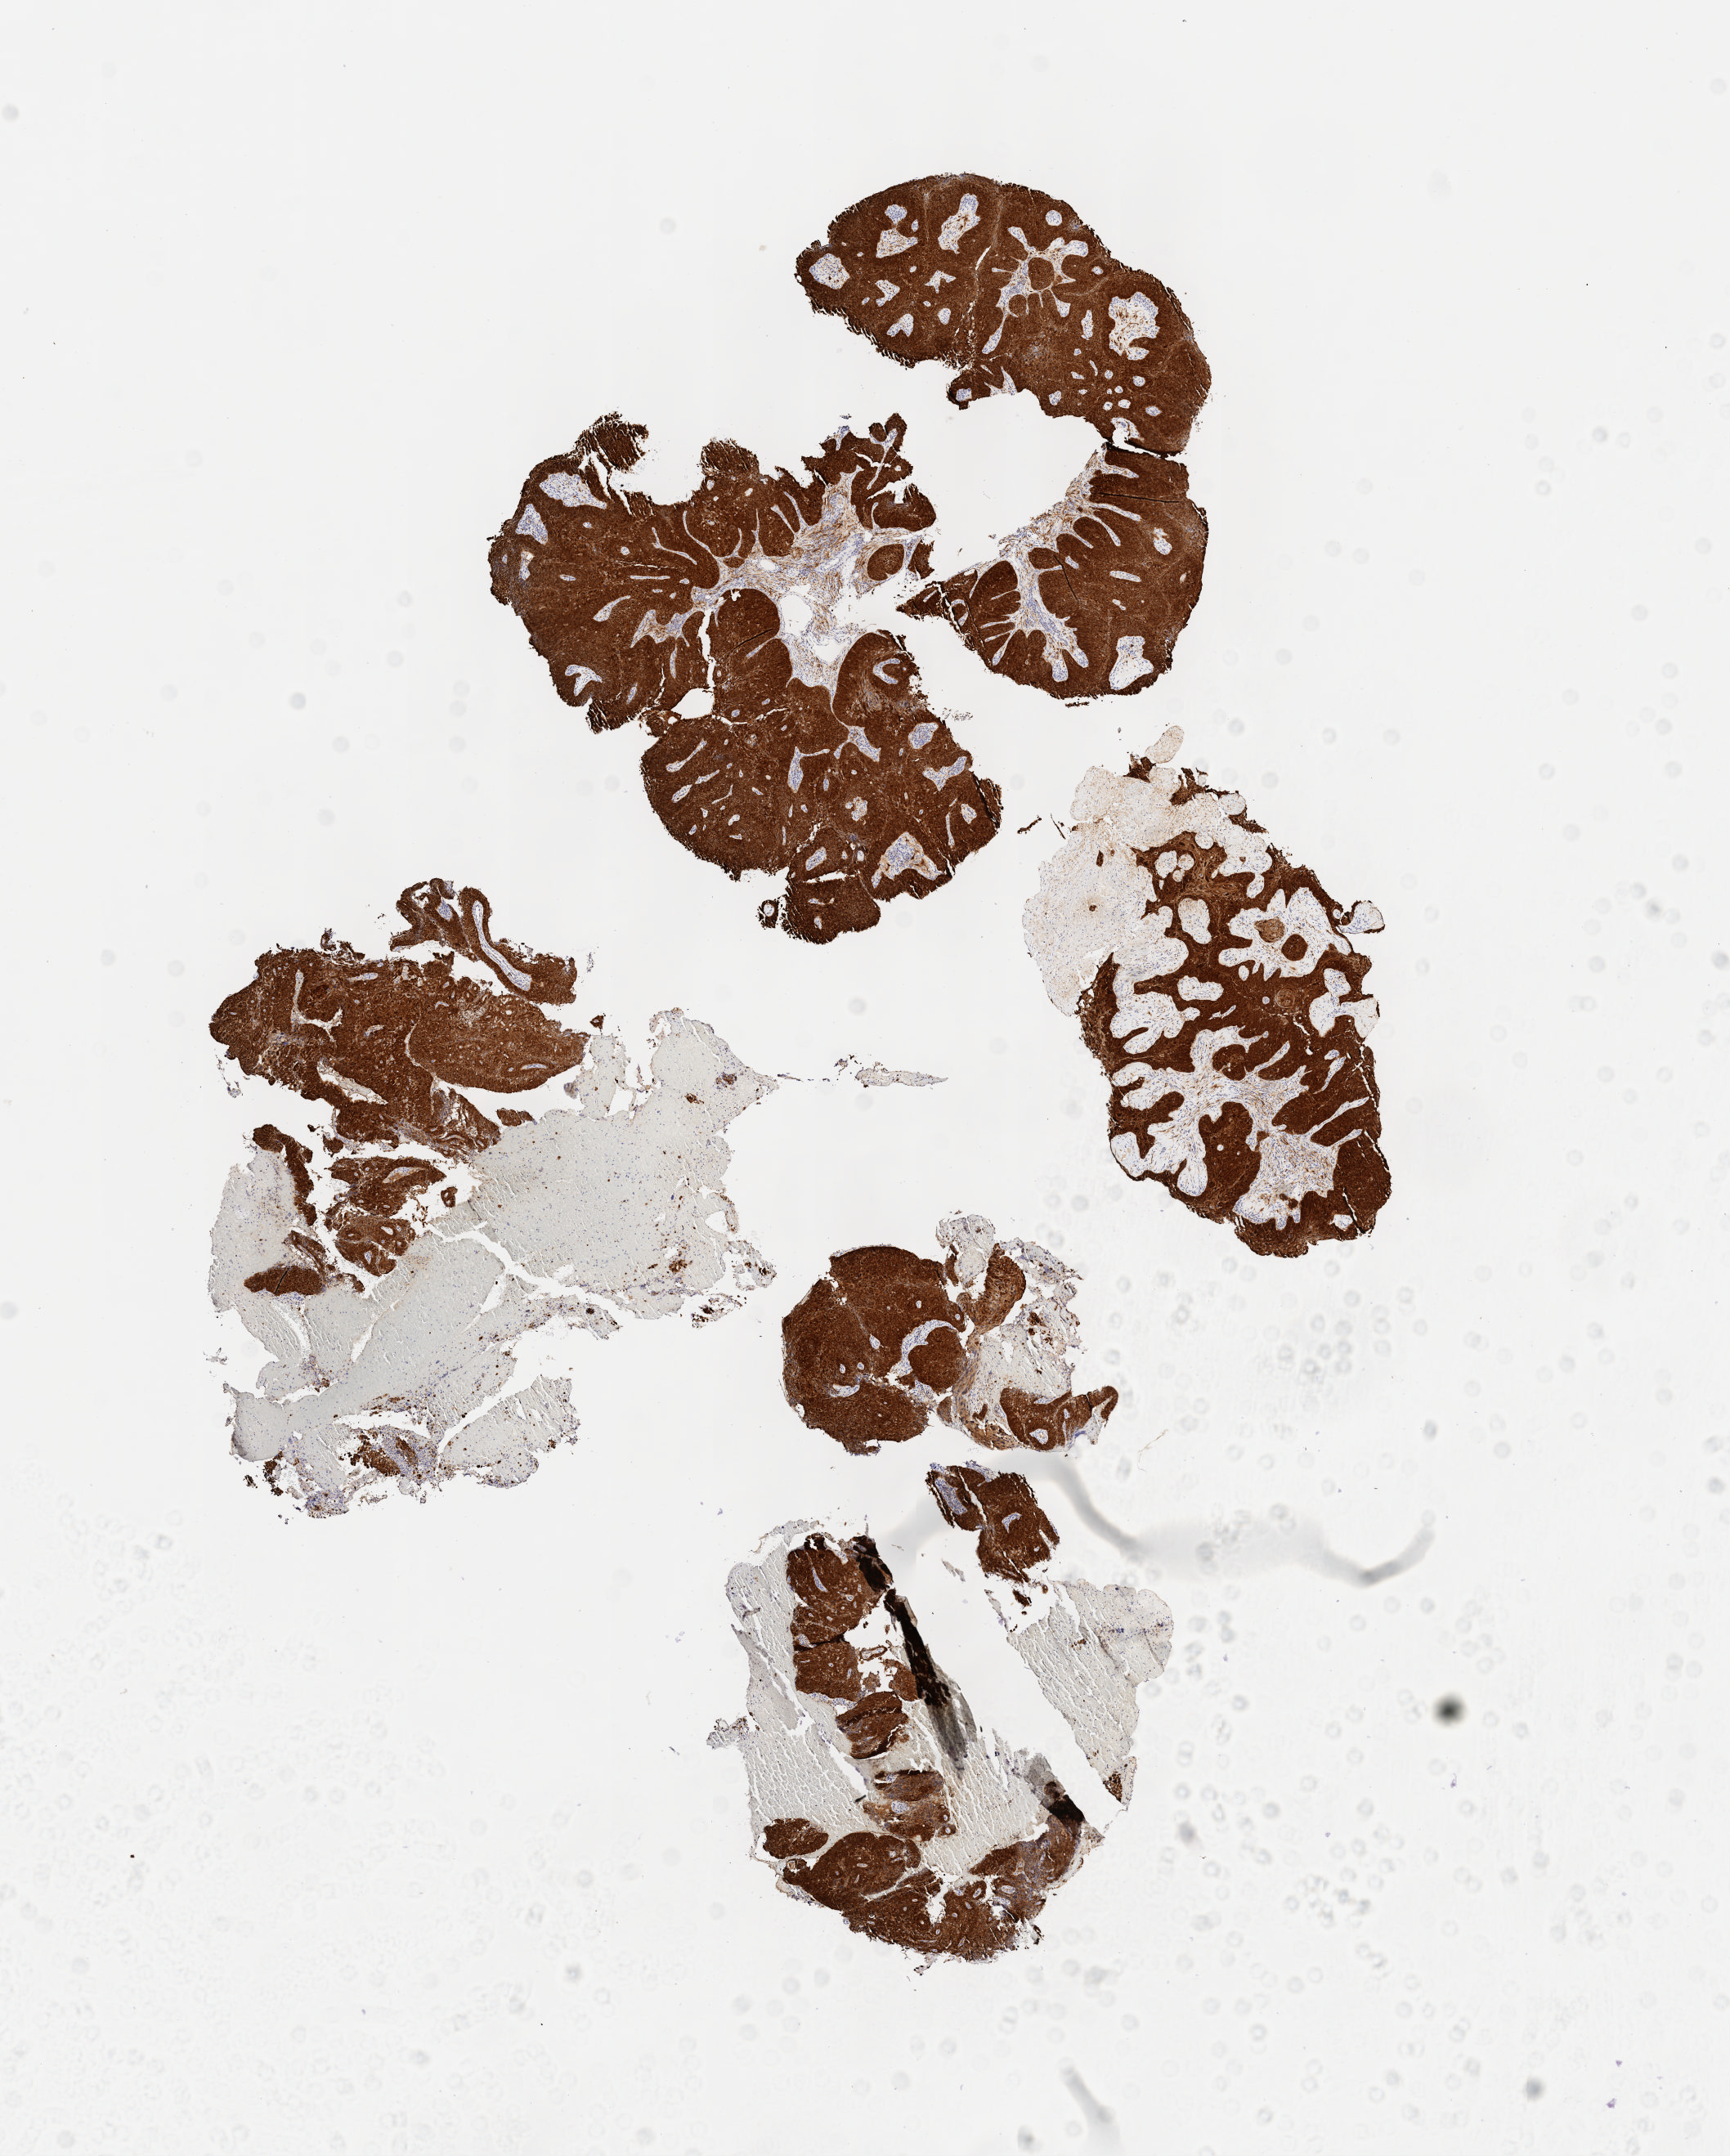
Immunohistochemistry (IHC) whole-slide image stained for p16 (p16INK4a), whole scanned area (about 8.6 x 10.7 mm) shown as a low-resolution overview. Tumor tissue. Anatomic site: cervix. Patient: female, 59 years old.
• diagnosis: Squamous cell carcinoma, large cell, nonkeratinizing, NOS